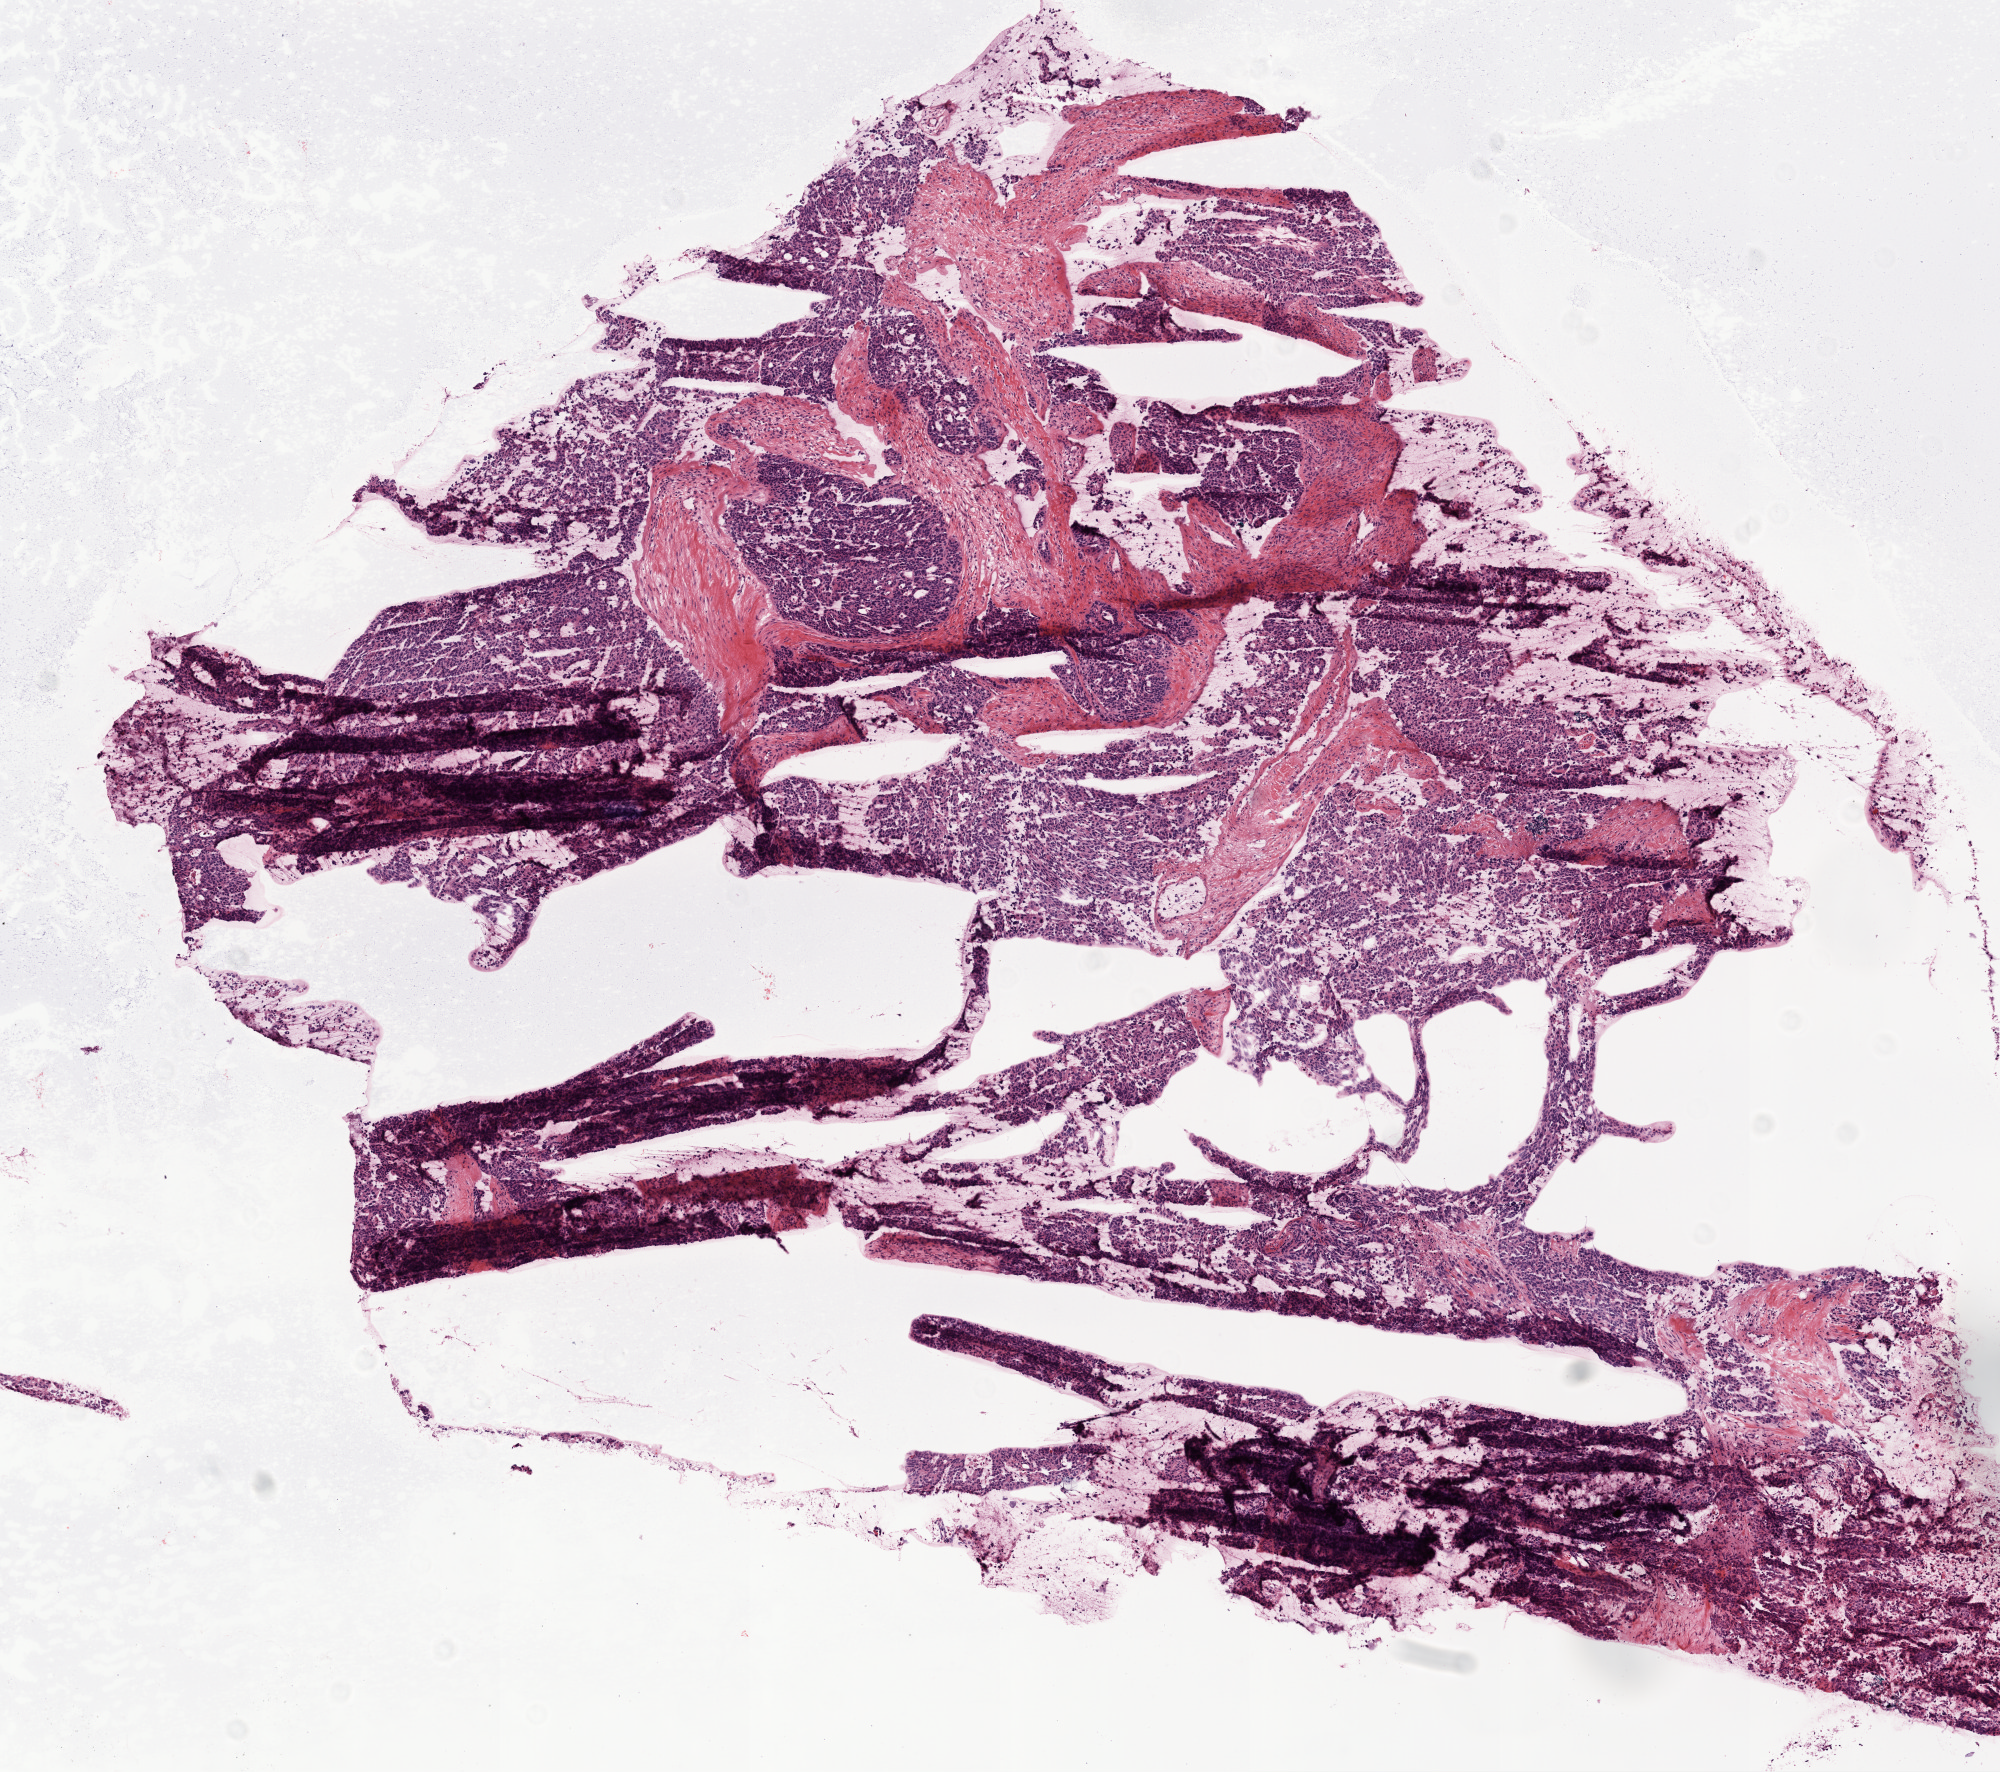
H&E-stained whole-slide image, low-resolution overview of the scanned area, about 8.0 x 7.1 mm; frozen section from the top of the tissue portion; sample: primary tumour, ovary. Female, age 51 years at initial diagnosis. Histologic grade: G3 (poorly differentiated). Composition of this section per pathologist review: tumour cells 77%, tumour nuclei 95%, normal cells 0%, stromal cells 20%, necrosis 3%.
* FIGO stage: IIIC
* laterality: bilateral
* histologic diagnosis: Serous cystadenocarcinoma, NOS